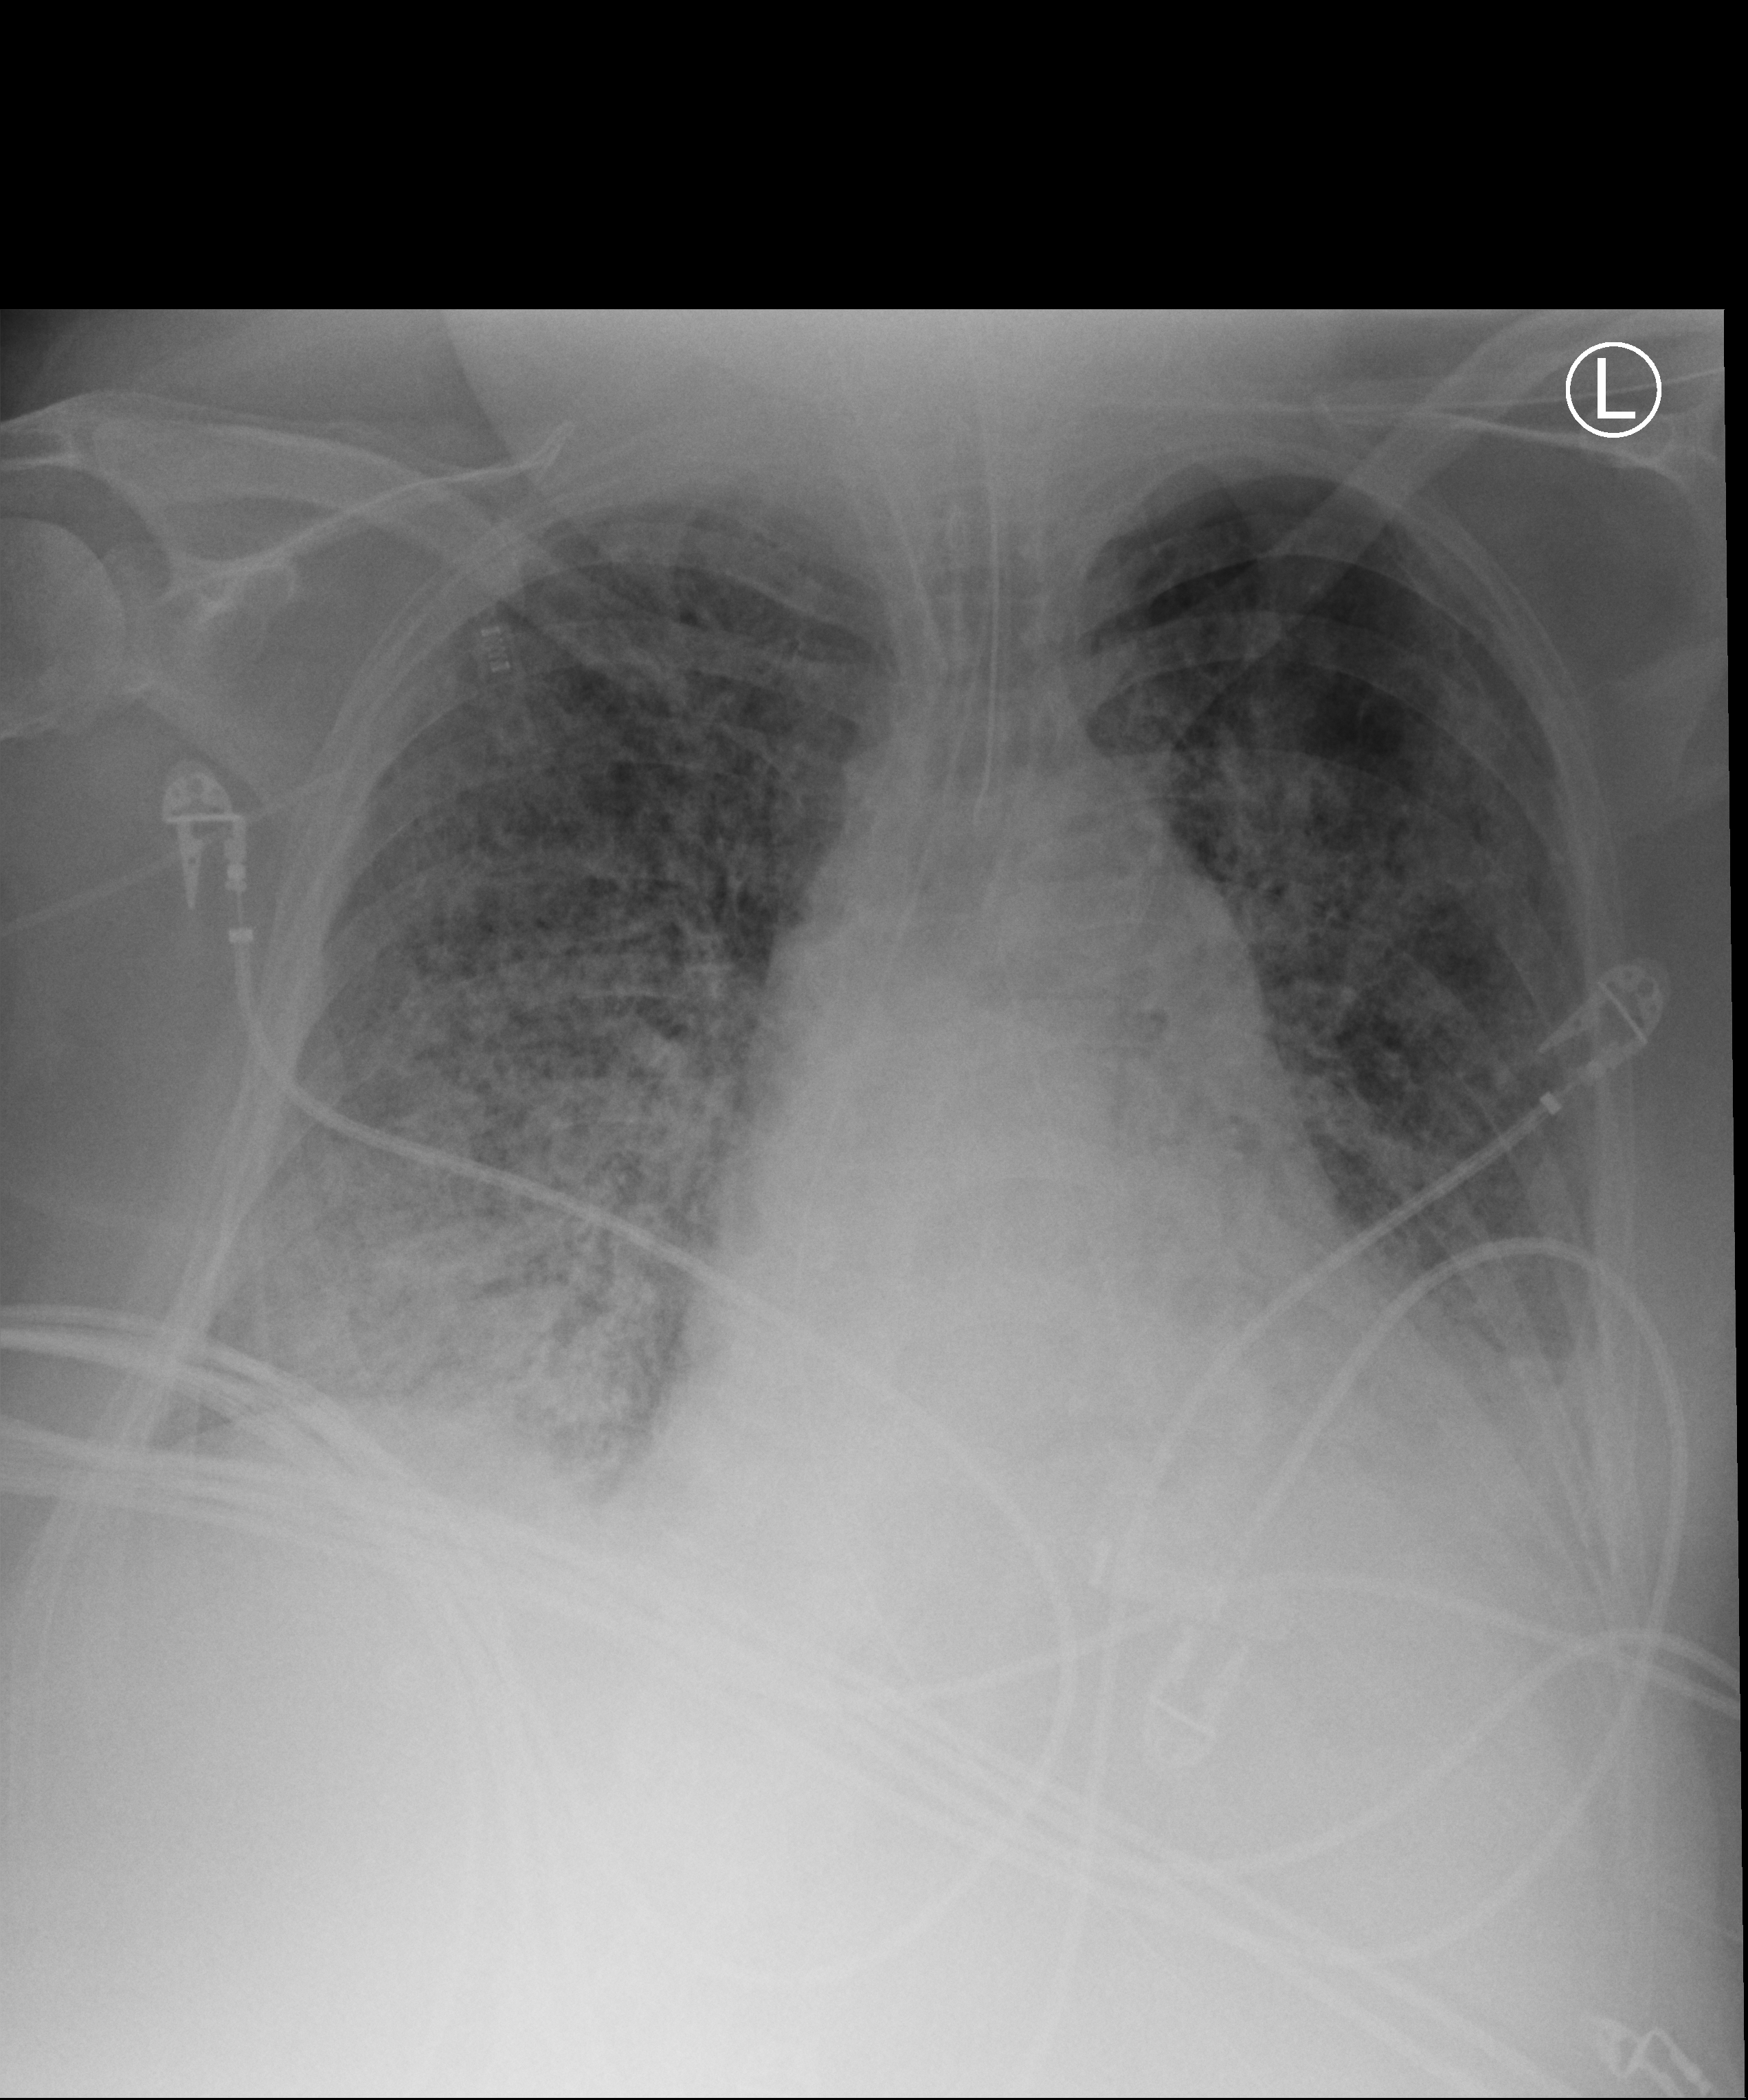
Portable chest radiograph, anteroposterior (AP) projection. Female patient hospitalised with COVID-19, age 60–74 years.
Hospital-stay facts (about this admission, not read from this image; timing relative to this image not recorded): smoking status (admission record): former; hypertension (admission record): yes; mechanically ventilated during this hospital stay: yes.